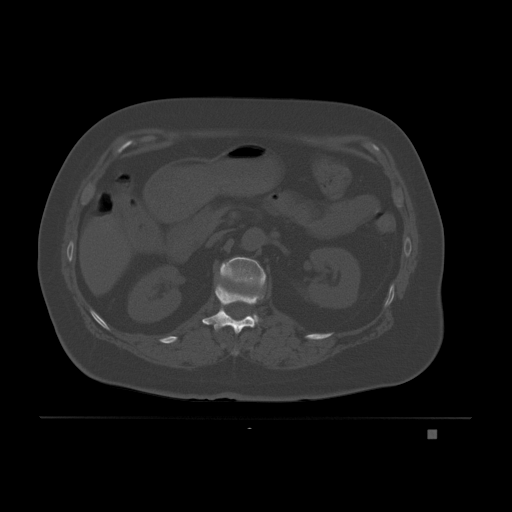
CT including the spine, one axial slice. Slice 78 of 221 in the series (ordered by position). Bone window (W 1800 / L 400 HU). 3 mm slice thickness. 512 × 512 image matrix, field of view 474 × 474 mm. Patient: female, 63 years. From the clinical record (not read from this slice): primary cancer: breast.
Structures marked on this image (semi-automatic segmentation, software-assisted and operator-edited):
- L1 vertebra: box from (x=219, y=257) to (x=266, y=324) px
- T11 vertebra: (x=232, y=351)–(x=239, y=355)
- T12 vertebra: (x=202, y=284)–(x=258, y=334)